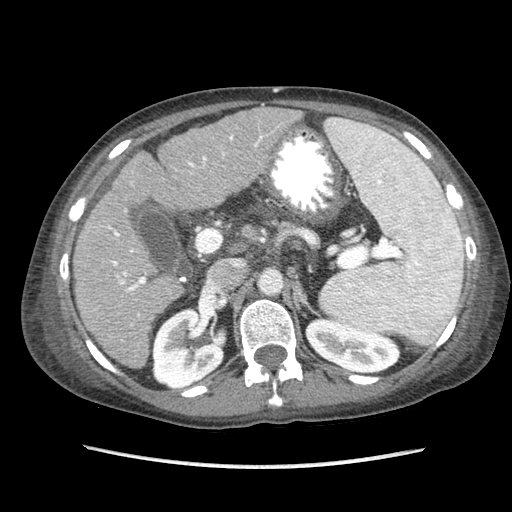
Contrast-enhanced abdominal CT (liver protocol), one axial slice. Slice 44 of 87 in the series (ordered by position). Reconstruction kernel STANDARD. 120 kVp. Soft-tissue window (W 400 / L 40 HU). 2.5 mm slice thickness. 512 × 512 image matrix, field of view 340 × 340 mm. Case-level facts recorded for this patient, not image findings: diagnosis: hepatocellular carcinoma (patient treated with transarterial chemoembolisation; whether this scan precedes or follows treatment is not stated here); TNM stage (as recorded): Stage-IIIB; Child-Pugh class: A; tumour differentiation: no biopsy.
Annotated regions visible in this slice (semi-automatic segmentation, software-assisted and operator-edited):
- liver parenchyma outside the tumour (the mass and vessels are separate outlines, so this box may not span the whole liver): bounding box <72,106,302,368> (left, top, right, bottom; pixels)
- liver vessels: <108,135,263,292>